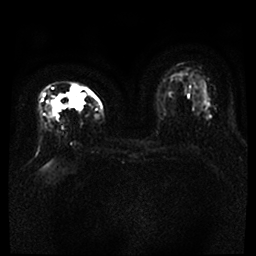
Breast MRI, one axial slice; position 22 of 46 along the scan axis; diffusion-weighted series; image 2 of 4 stored at this slice position (different b-values; order by instance number); 1.5 T; 4 mm slice thickness; 256 × 256 image matrix. Female patient.
Structures marked on this image (outlined manually by an expert reader):
- tumour on diffusion-weighted imaging: bounding box <52,85,85,111> (left, top, right, bottom; pixels)